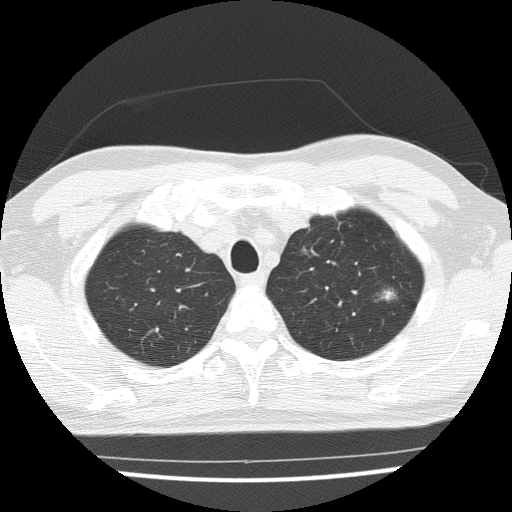
Low-dose screening chest CT, one axial slice; position 124 of 154 along the scan axis; reconstruction kernel FC51; lung window (W 1500 / L -600 HU); 512 × 512 image matrix, field of view 330 × 330 mm.
Structures marked on this image (outlined manually by an expert reader):
- lesion 1 (tumor, upper lobe of left lung): bounding box <381,291,394,300> (left, top, right, bottom; pixels)